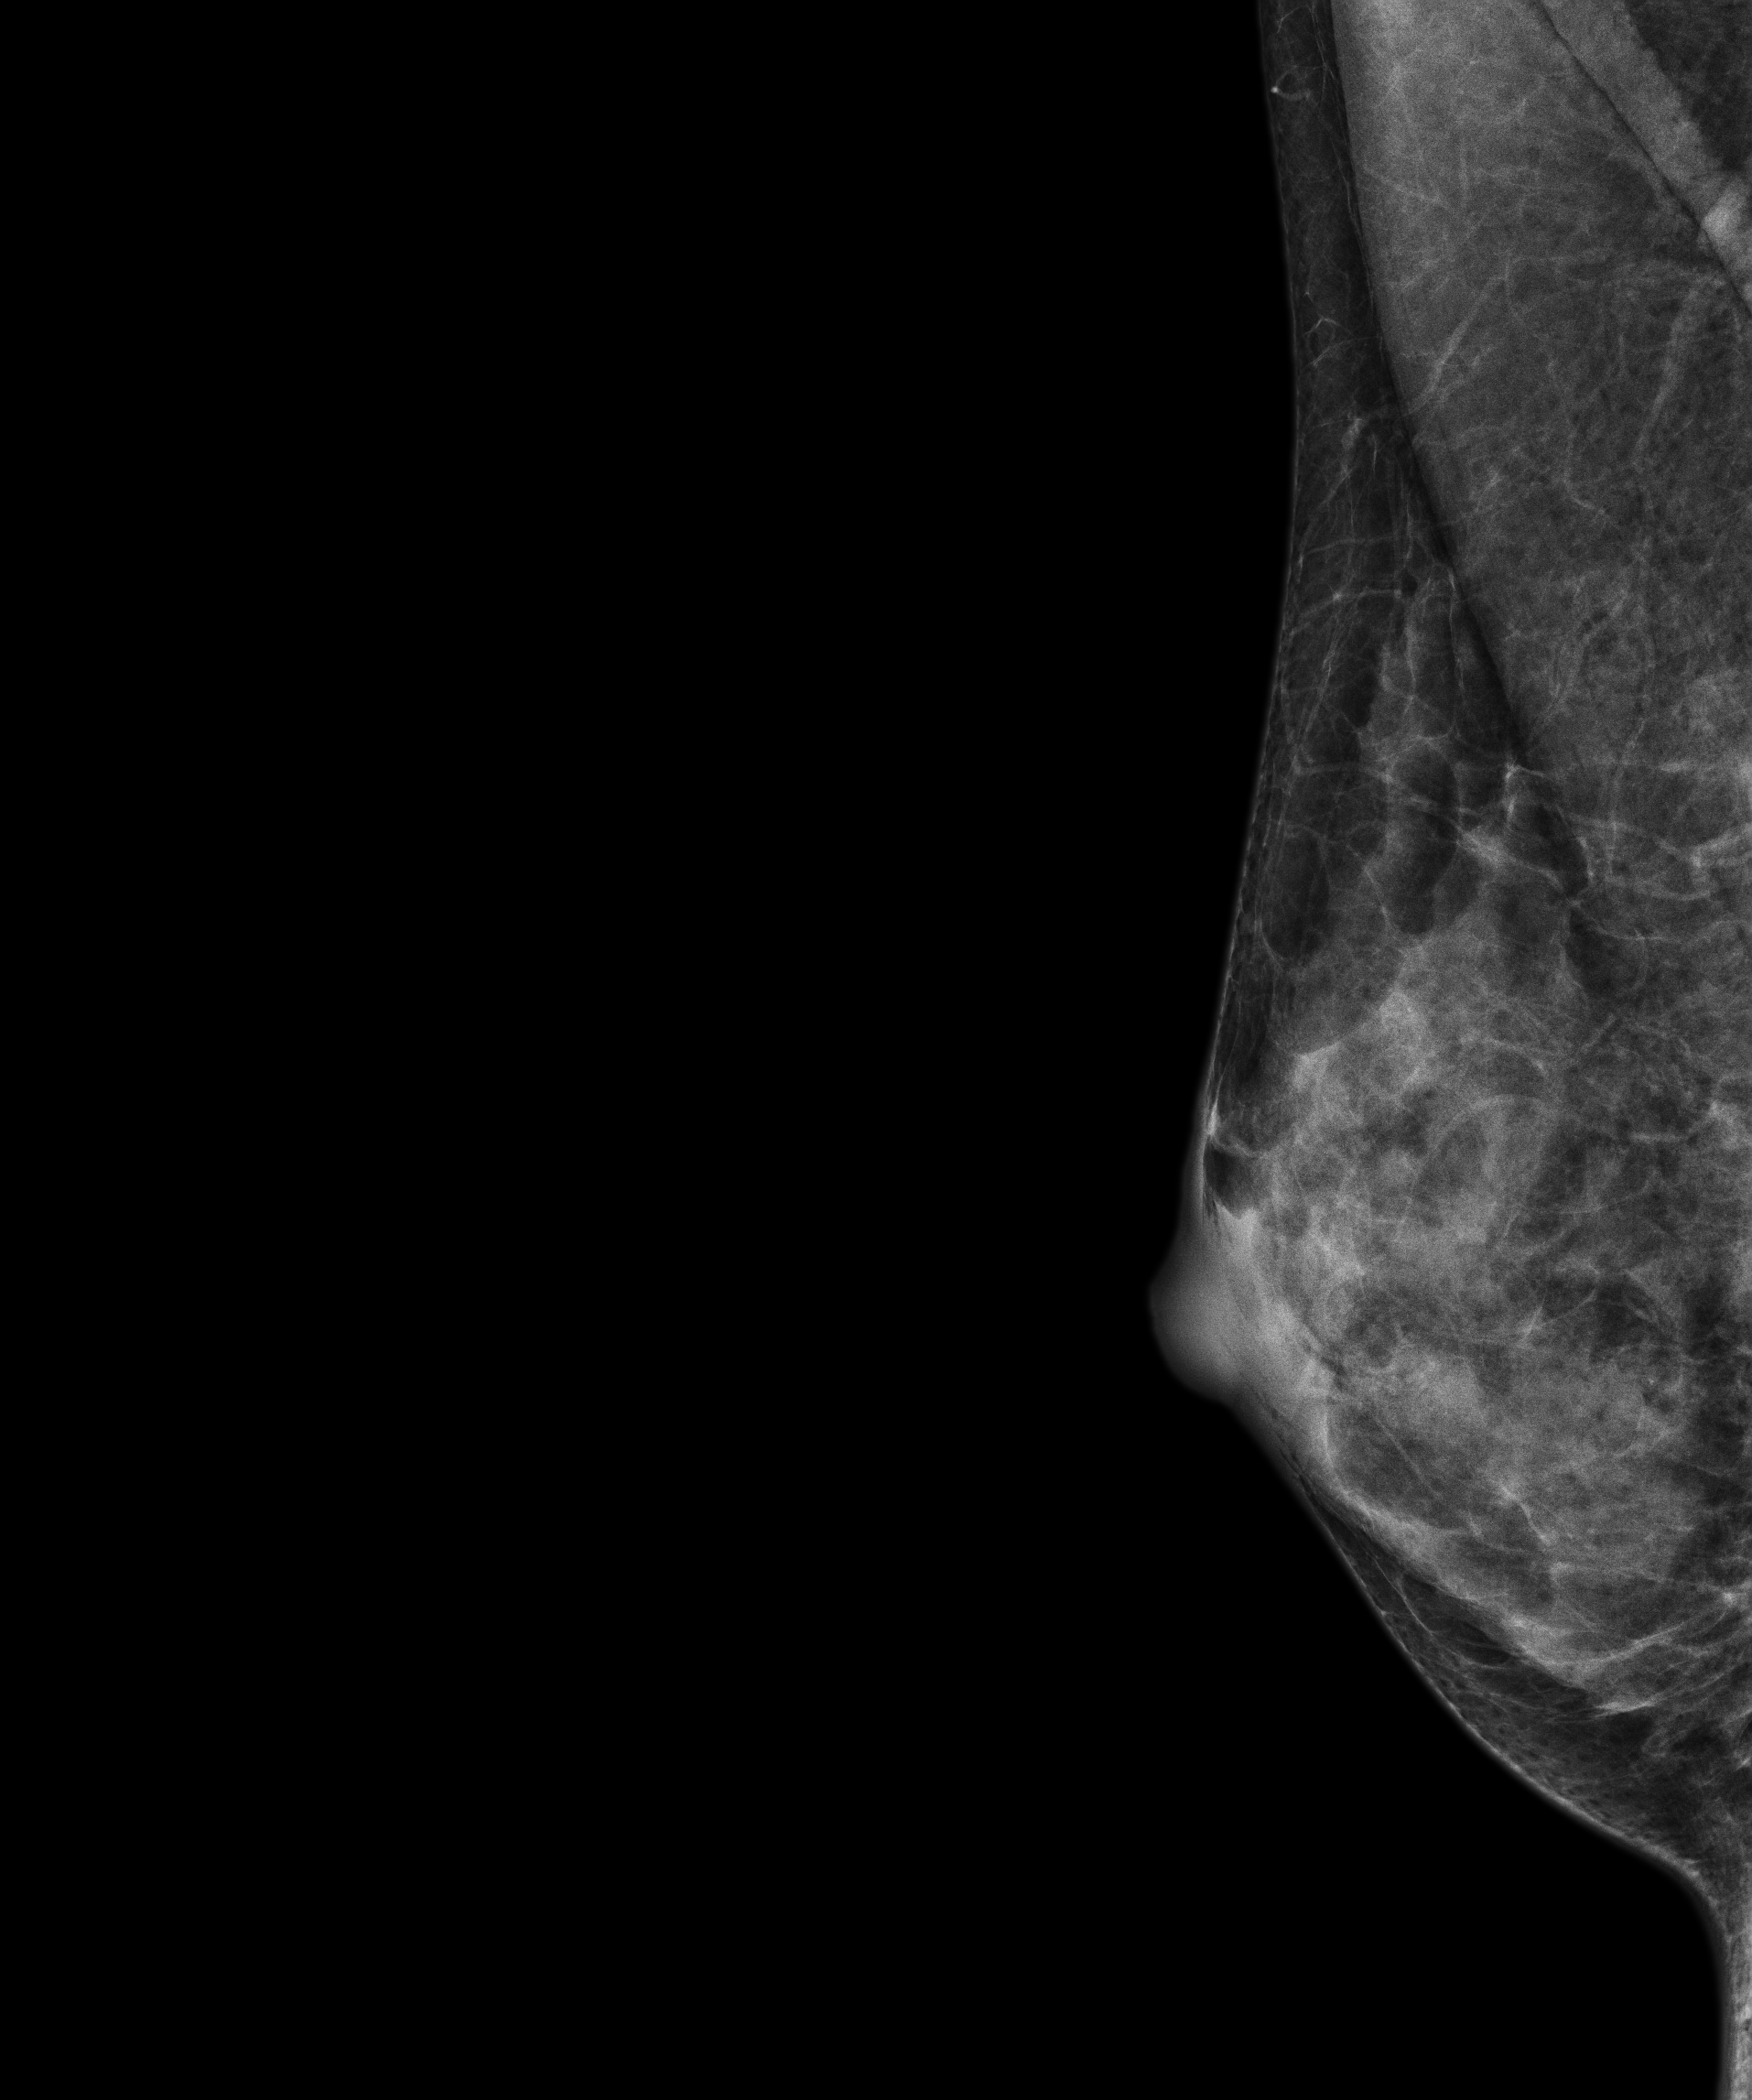
Screening examination, system: Senographe Pristina. Patient: female, 47 years.
Image type: full-field digital mammogram. Breast: right. Projection: mediolateral oblique (MLO) view.